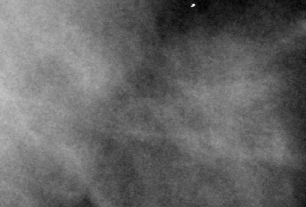
Cropped region of a digitized screen-film mammogram centred on a radiologist-marked abnormality; left breast; MLO view; BI-RADS breast density category 3 (scale 1–4).
Finding: mass, shape irregular, margins ill defined / spiculated; BI-RADS assessment category 4; pathology (as recorded): malignant.